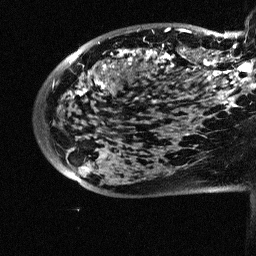
Breast MRI (dynamic contrast-enhanced), one sagittal slice; slice 16 of 64 in the series (ordered by position); dynamic contrast-enhanced study with each time point stored as its own series, time point 2 of 3 at this slice position (early post-contrast, ordered by acquisition time); 1.5 T; TE 4.5 ms, TR 11 ms; 2.5 mm slice thickness; 256 × 256 image matrix. Female patient, age 38 years. Case-level facts recorded for this patient, not image findings: setting: breast cancer imaged before/during neoadjuvant chemotherapy; receptor status: HR-positive, HER2-negative.
Outlined on this slice (semi-automatic segmentation, software-assisted and operator-edited):
- analysis volume of interest (the breast-tissue region the enhancement analysis was run in; not a lesion): bounding box <88,18,252,126> (left, top, right, bottom; pixels)
- tumour enhancement mask (voxels above the 90 % enhancement threshold inside the analysis volume of interest): <110,28,252,113>